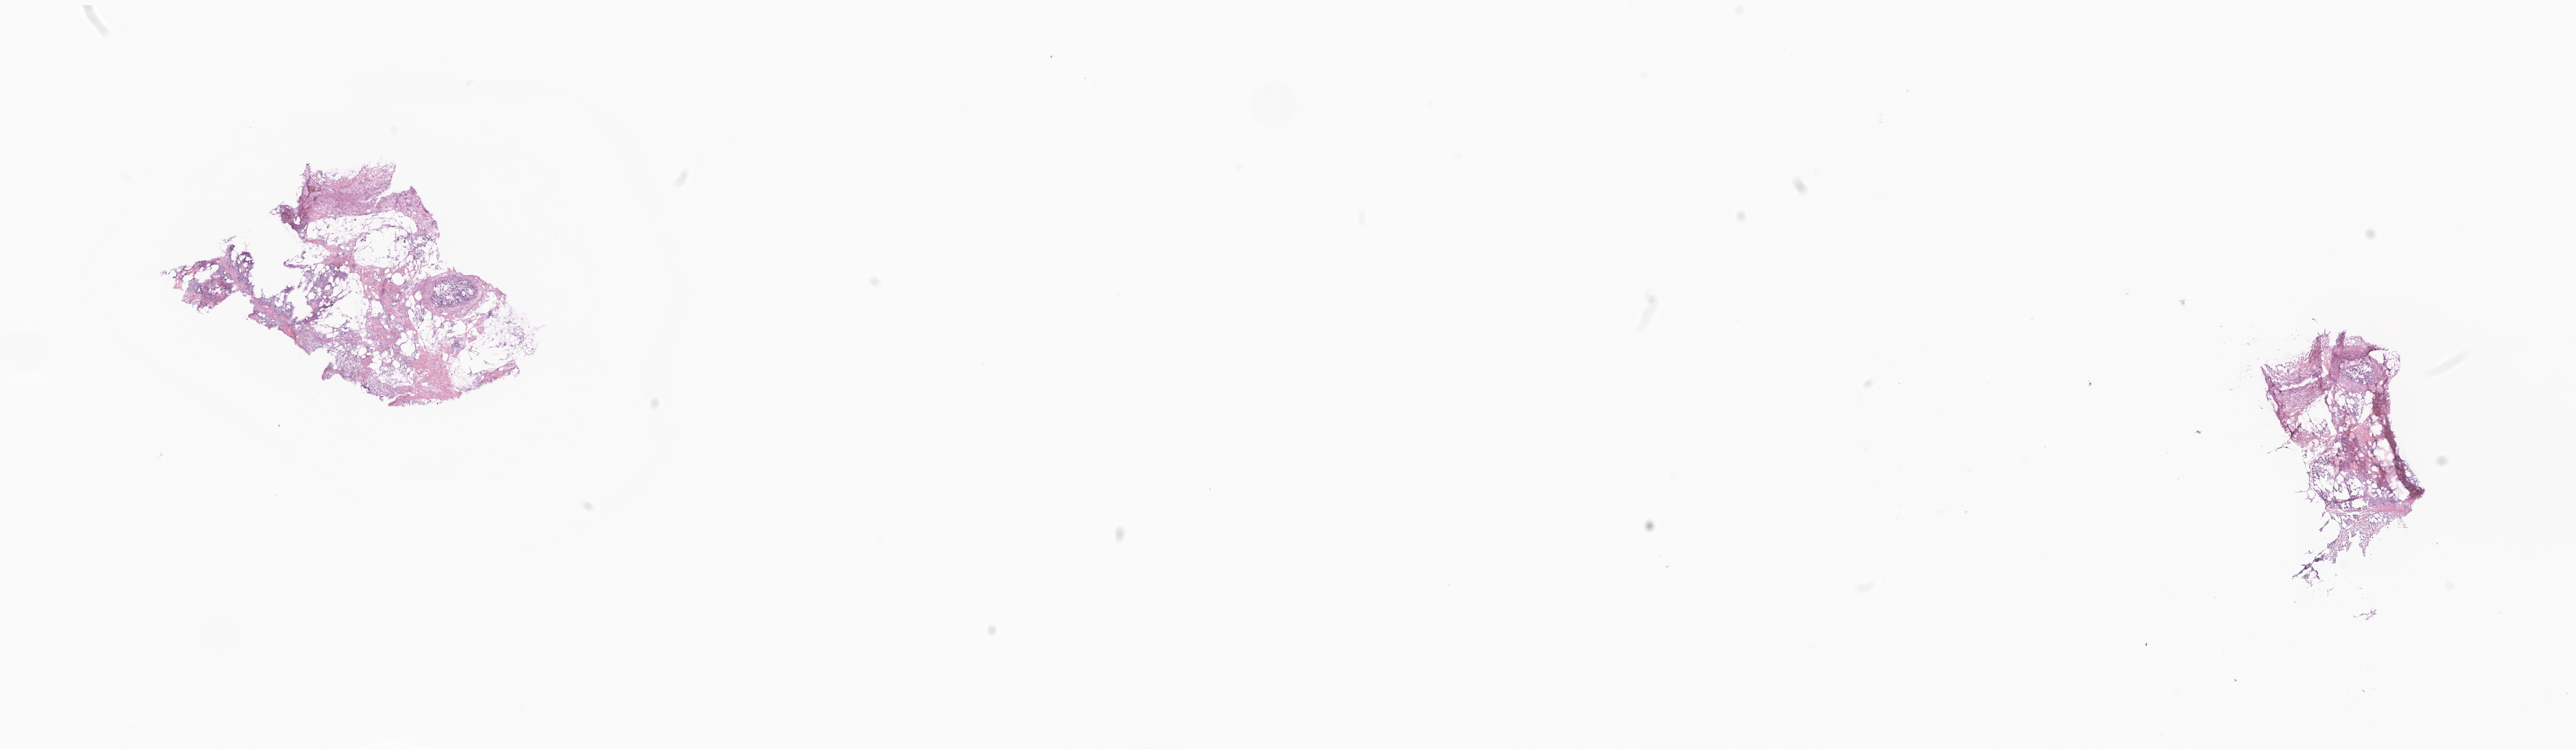
Digitized hematoxylin and eosin (H&E)-stained section, shown as a low-resolution overview of the whole scanned area (about 29.9 x 8.7 mm); frozen section (tissue freezing medium); primary tumor; site: breast (left). Female patient; age at initial diagnosis 66 years. Slide review estimates, as recorded: tumor cells 100%, tumor nuclei 70%, stromal cells 0%, necrosis 0%, normal cells 0%. Infiltration values recorded for this section: lymphocyte infiltration 0%, monocyte infiltration 0%, neutrophil infiltration 0%.
Histologic diagnosis: Infiltrating duct carcinoma, NOS.